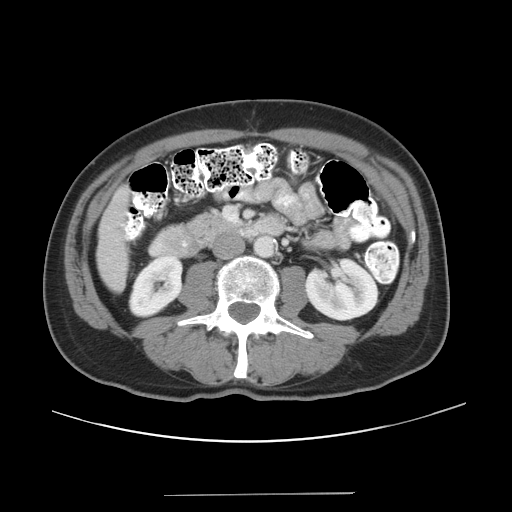
Contrast-enhanced abdominal CT, one axial slice. Reconstruction kernel STANDARD. 120 kVp. Soft-tissue window (W 400 / L 40 HU). 5 mm slice thickness. 512 × 512 image matrix, field of view 409 × 409 mm. Male patient, age 65 years. Case-level facts recorded for this patient, not image findings: diagnosis: colorectal cancer liver metastases, imaged before liver resection; multiple liver metastases: no; largest metastasis: 3.8 cm; disease in both lobes: no.
Structures marked on this image (expert manual segmentation):
- liver: bounding box [x1, y1, x2, y2] px = [98, 192, 127, 290]
- planned liver remnant (the part of the liver to remain after resection): [98, 192, 127, 290]